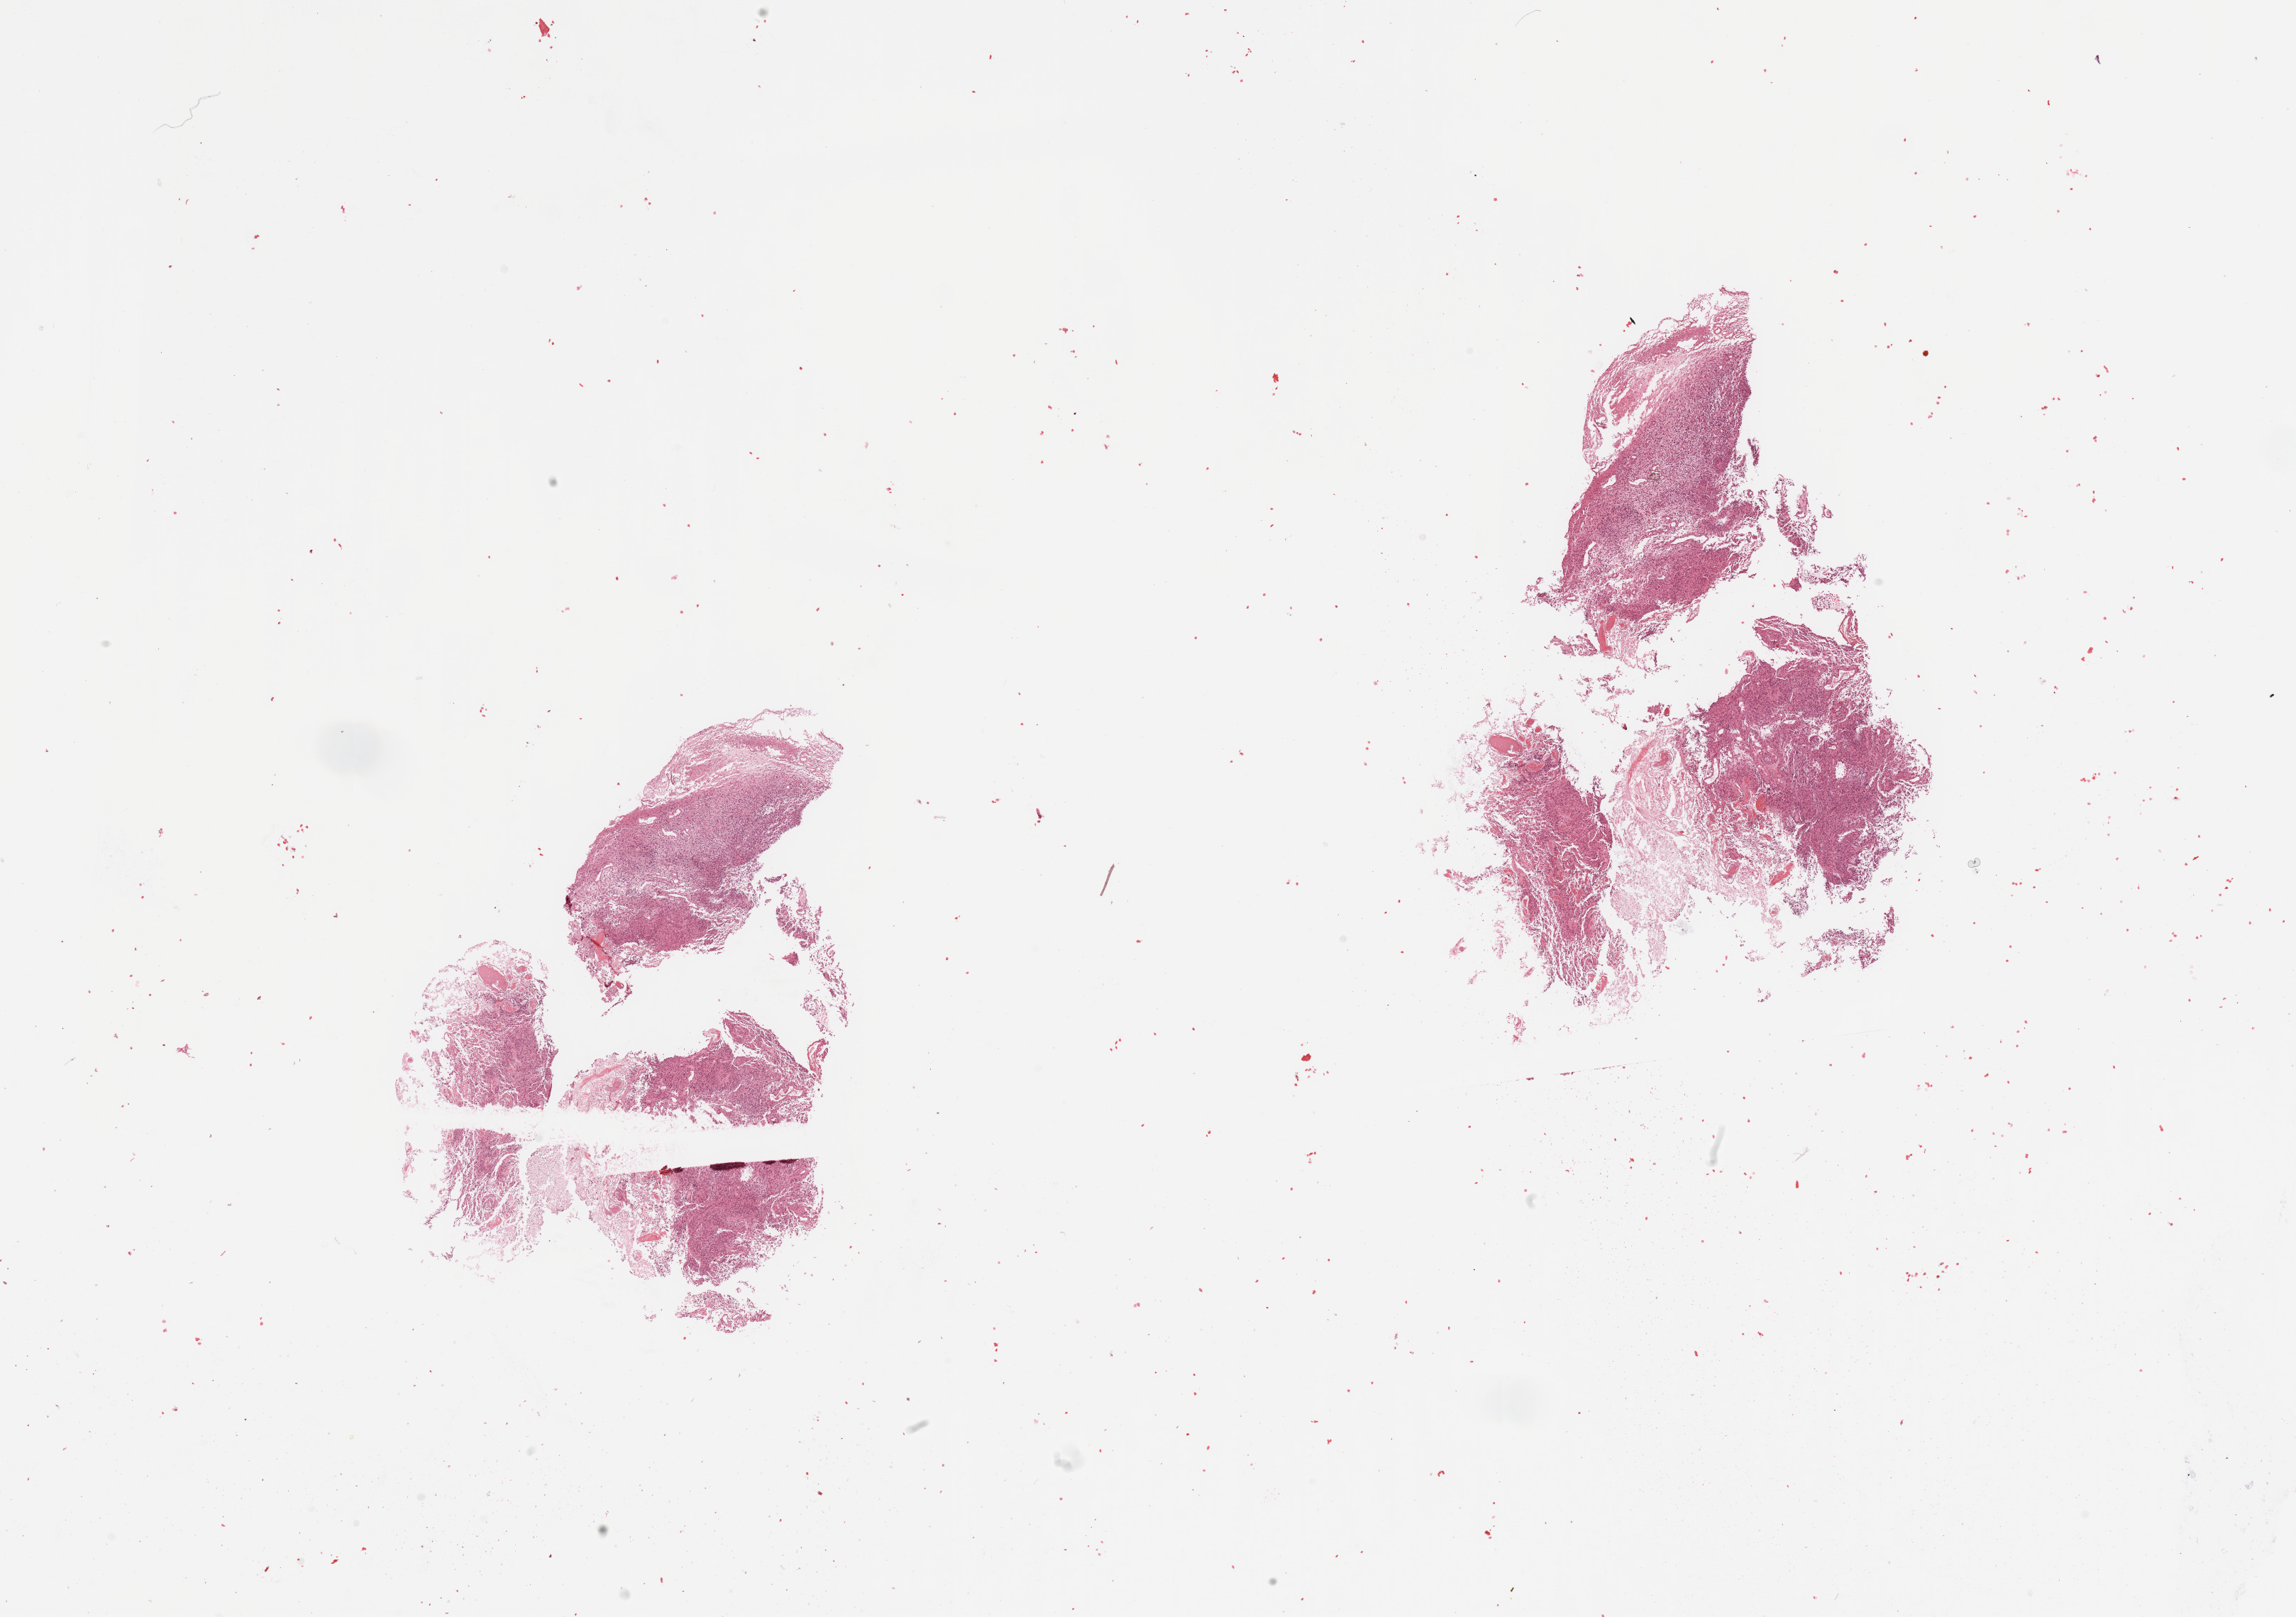
Whole-slide histology image, H&E — a low-resolution overview of the entire scanned area, about 25.6 x 18.0 mm. Brain, tumour tissue. 77-year-old female patient.
Primary tumour site (as recorded): temporal lobe. Diagnosis: Glioblastoma.